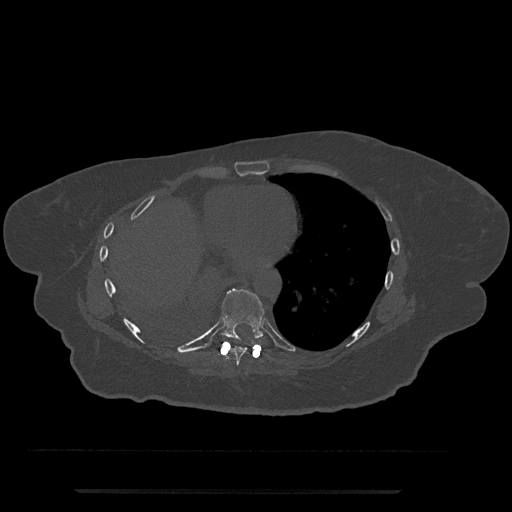
CT including the spine, one axial slice; reconstruction kernel Br40s/3; 120 kVp; bone window (W 1800 / L 400 HU); 0.5 mm slice thickness; 512 × 512 image matrix, field of view 440 × 440 mm. Female patient, age 51 years. From the clinical record (not read from this slice): primary cancer: neuro; vertebrae with lytic lesions (as recorded): T8.
Structures marked on this image (semi-automatic segmentation, software-assisted and operator-edited):
- T8 vertebra: bounding box [x1, y1, x2, y2] px = [229, 346, 247, 366]
- T9 vertebra: [214, 289, 265, 342]